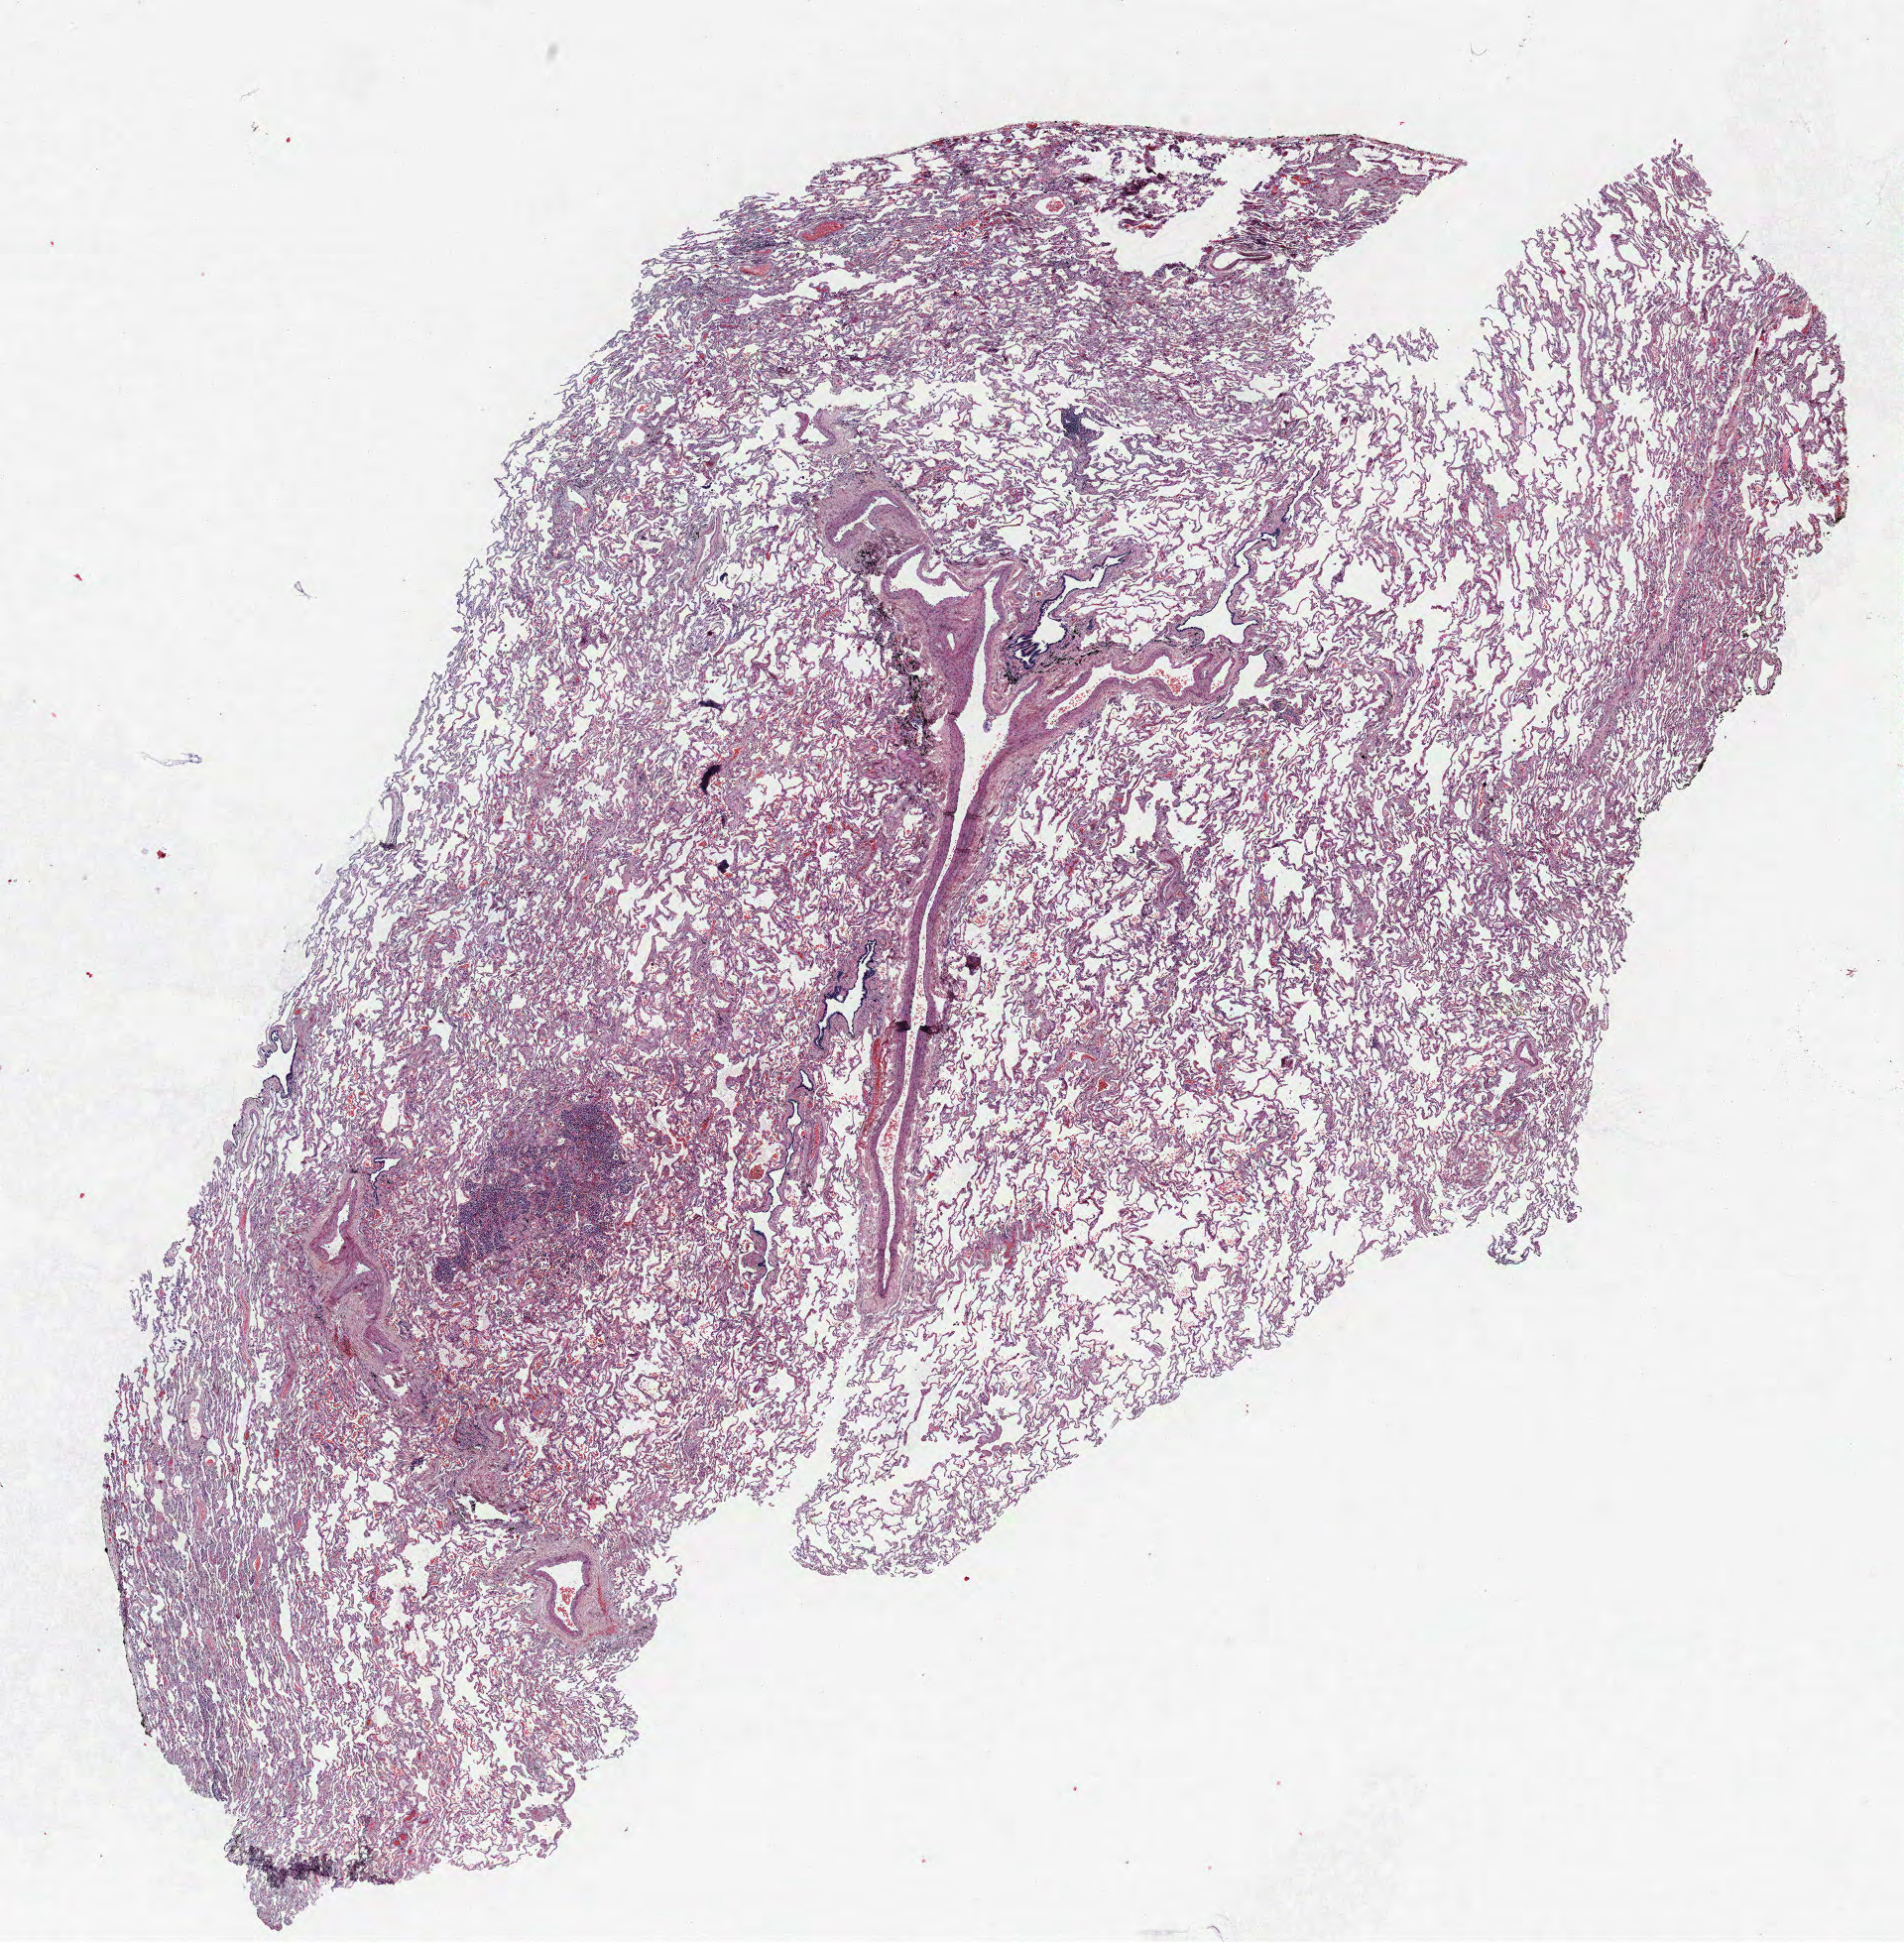
H&E-stained whole-slide image, a low-resolution overview of the entire scanned area, about 15.4 x 15.7 mm (slide scanned at 40x). FFPE section. Lung. Male patient, aged 74 at enrolment. Former smoker at enrolment.
Participant's lung-cancer diagnosis: Bronchiolo-alveolar carcinoma, non-mucinous.